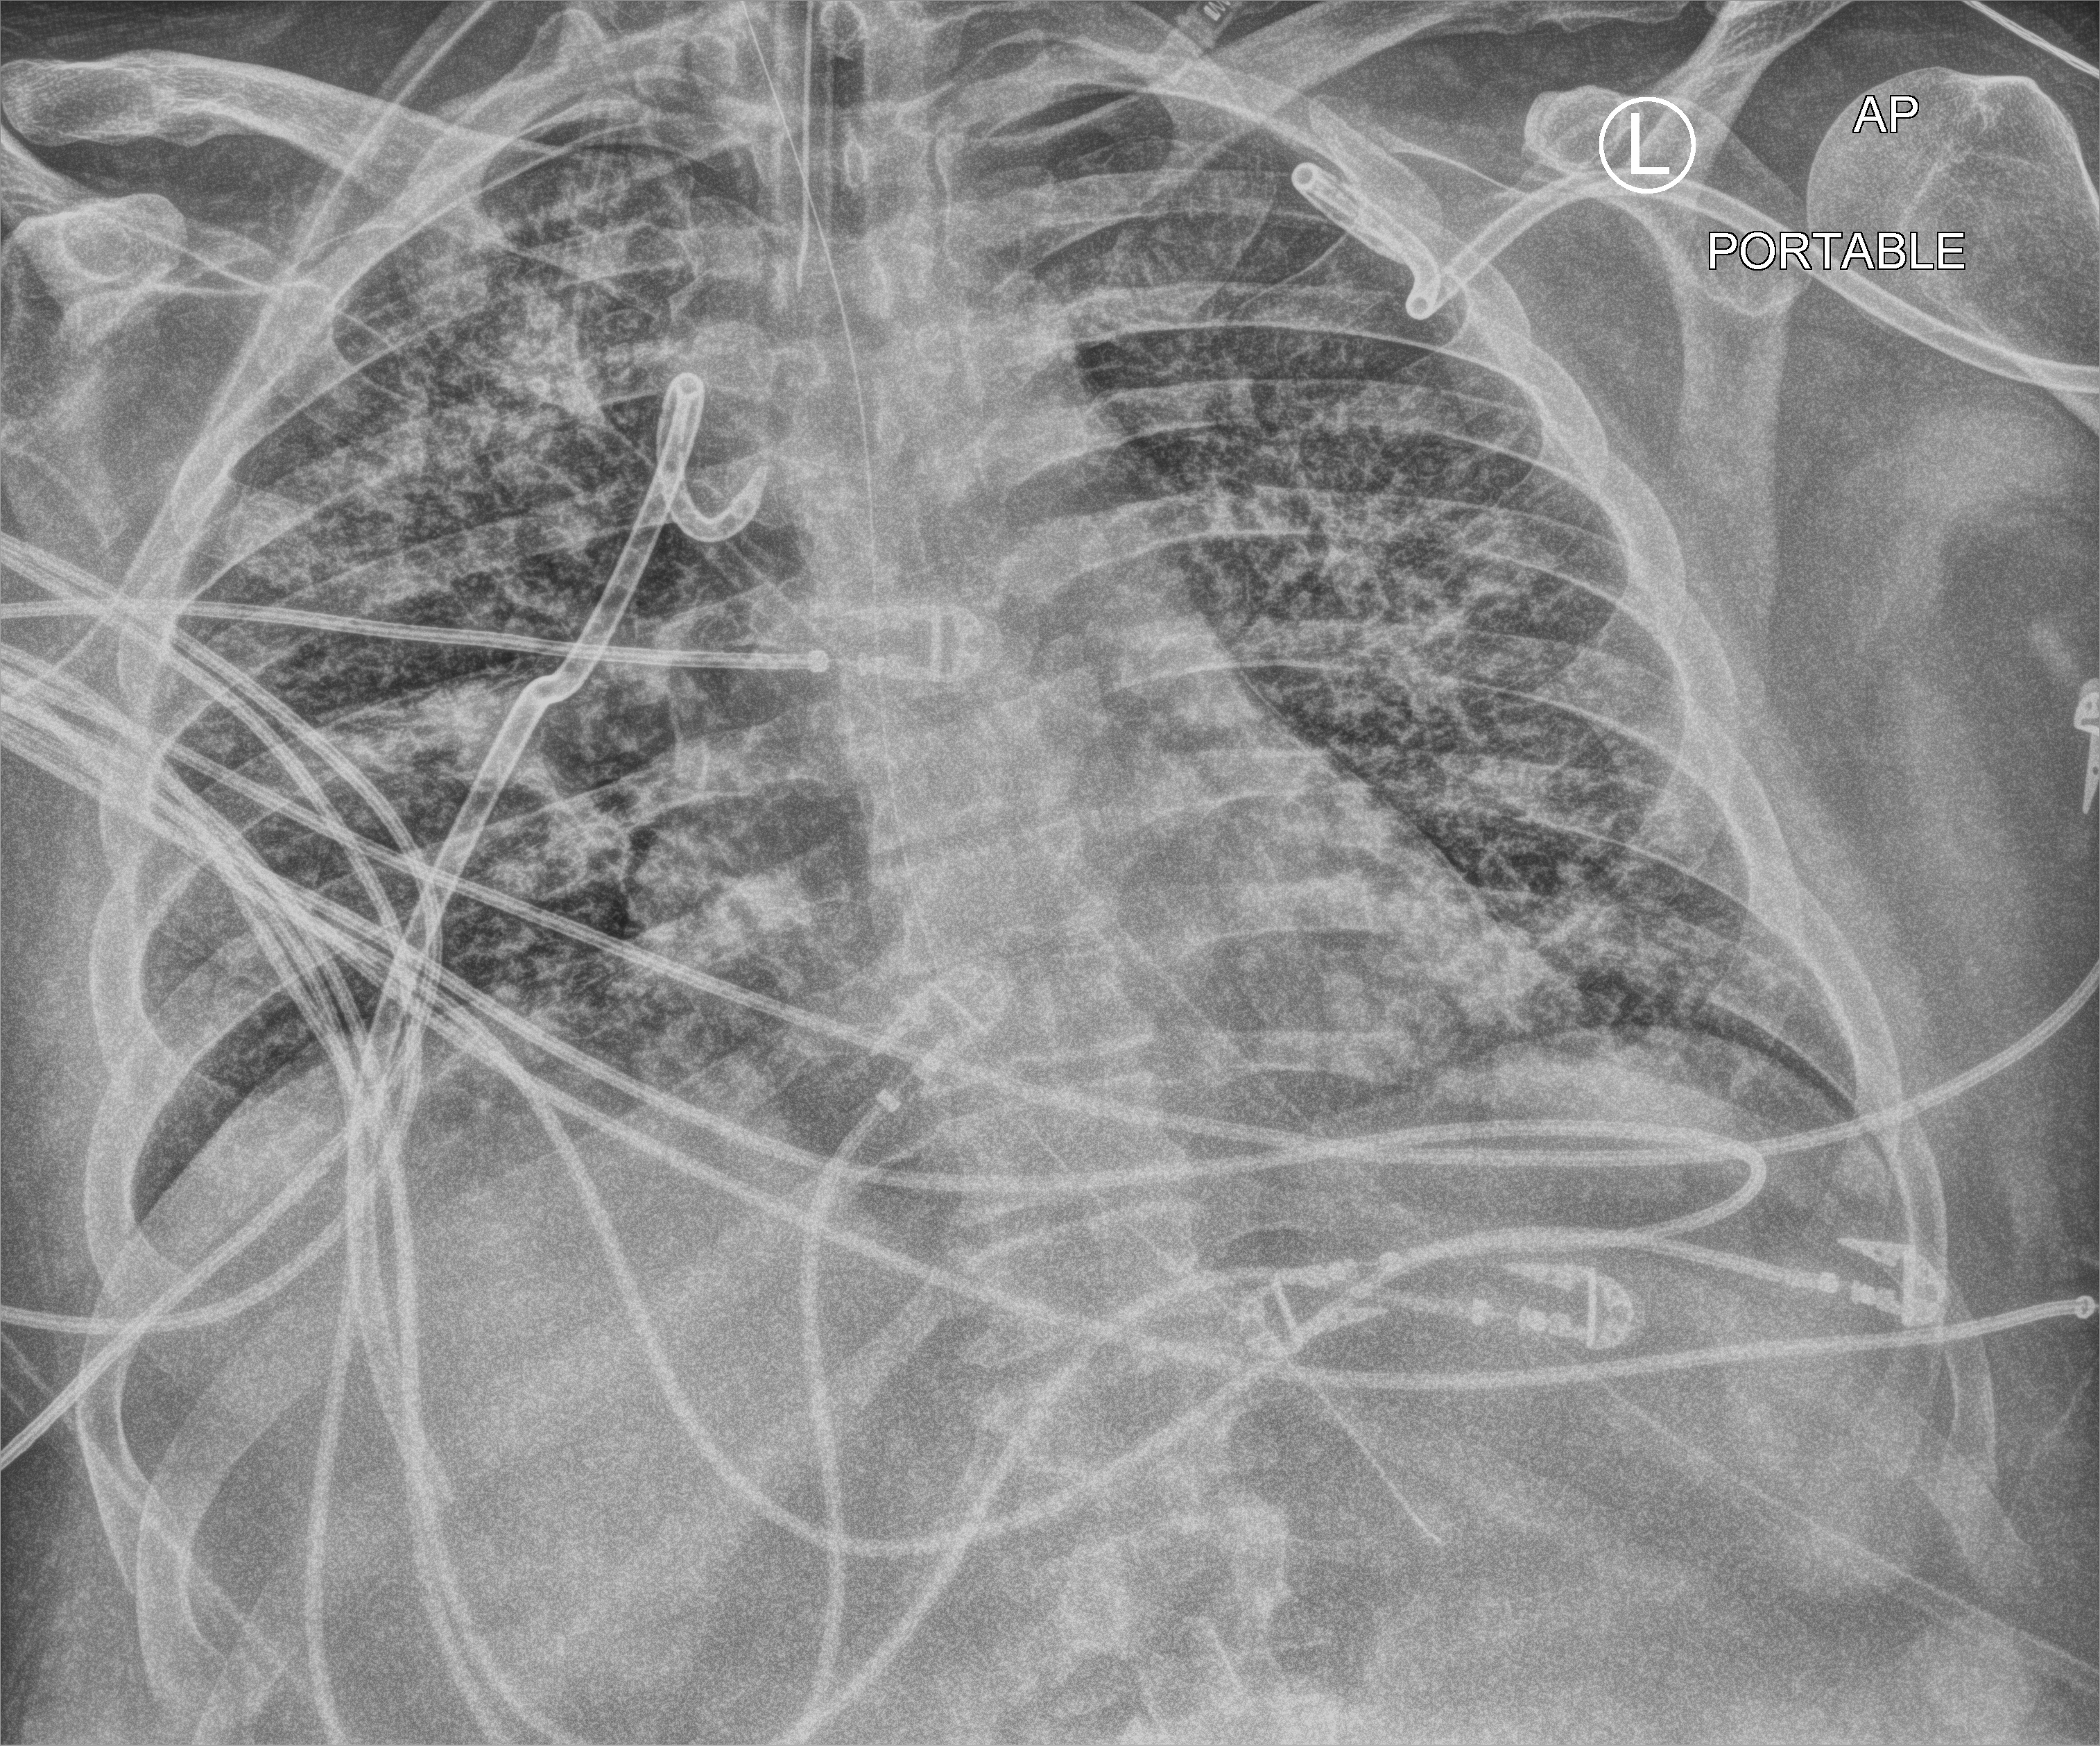
Portable chest radiograph; anteroposterior (AP) projection. Adult patient hospitalised with COVID-19, age 18–59 years.
From the hospital-stay record, not from the radiograph (when in the stay this image was taken is not recorded): admitted to intensive care during this hospital stay: yes; mechanically ventilated during this hospital stay: yes.